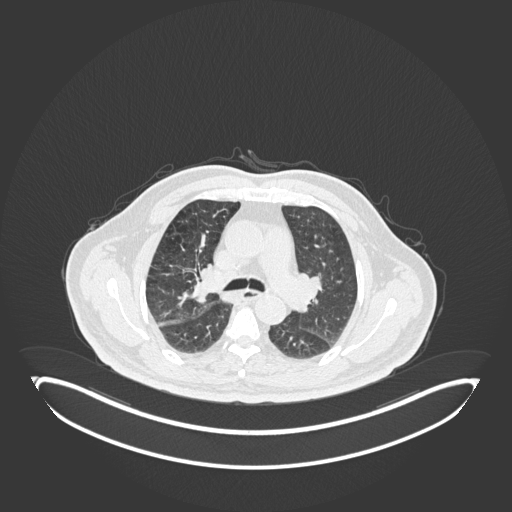
Chest CT, one axial slice; slice 116 of 247 in the series (ordered by position); 120 kVp; lung window (W 1500 / L -600 HU); 1 mm slice thickness; 512 × 512 image matrix. Patient: male, 72 years. Case-level facts recorded for this patient, not image findings: clinical TNM (as recorded): T1c N0 M0.
Structures marked on this image (rectangle marked by the reading radiologist):
- lung tumour (recorded histology: squamous cell carcinoma): bounding box [x1, y1, x2, y2] px = [183, 258, 216, 312]